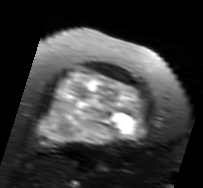
MRI of an extremity soft-tissue mass, one axial slice. Slice 55 of 91 in the series (ordered by position). T2-weighted fat-saturated. MR volume resampled by the dataset authors to the PET/CT grid (not the native acquisition matrix). 203 × 188 image matrix. Female patient. Case-level facts recorded for this patient, not image findings: histological type: malignant solitary fibrous tumor; grade: intermediate; site of the primary tumour: right thigh.
Structures marked on this image (expert contour drawn on MRI and transferred to this co-registered scan by the dataset authors):
- gross tumour volume including surrounding oedema: bounding box [x1, y1, x2, y2] px = [37, 67, 148, 146]
- gross tumour volume (mass): [37, 69, 146, 146]